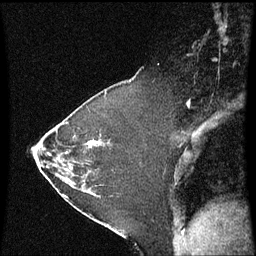
Breast MRI (dynamic contrast-enhanced), one sagittal slice; slice 39 of 60 in the series (ordered by position); dynamic contrast-enhanced series, image 2 of 3 at this slice position (ordered by acquisition); 1.5 T; TE 4.2 ms, TR 8.9 ms; 2 mm slice thickness; 256 × 256 image matrix. Patient: female, 37 years. From the clinical record (not read from this slice): setting: breast cancer imaged before/during neoadjuvant chemotherapy; receptor status: HR-positive, HER2-negative.
Annotated regions visible in this slice (semi-automatically segmented with operator editing):
- analysis volume of interest (the breast-tissue region the enhancement analysis was run in; not a lesion): bounding box <60,102,122,181> (left, top, right, bottom; pixels)
- tumour enhancement mask (voxels above the 70 % enhancement threshold inside the analysis volume of interest): <86,142,103,165>